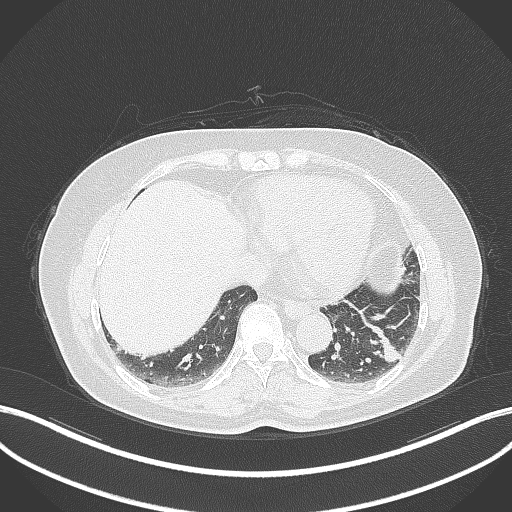
Chest CT, one axial slice. Slice 114 of 311 in the series (ordered by position). 120 kVp. Lung window (W 1500 / L -600 HU). 1 mm slice thickness. 512 × 512 image matrix, field of view 400 × 400 mm. Patient: female, 59 years. Case-level facts recorded for this patient, not image findings: clinical TNM (as recorded): T2a N0 M0; histopathological grade: G2-3.
Outlined on this slice (bounding box drawn by a radiologist):
- lung tumour (recorded histology: adenocarcinoma): box from (x=373, y=329) to (x=408, y=367) px